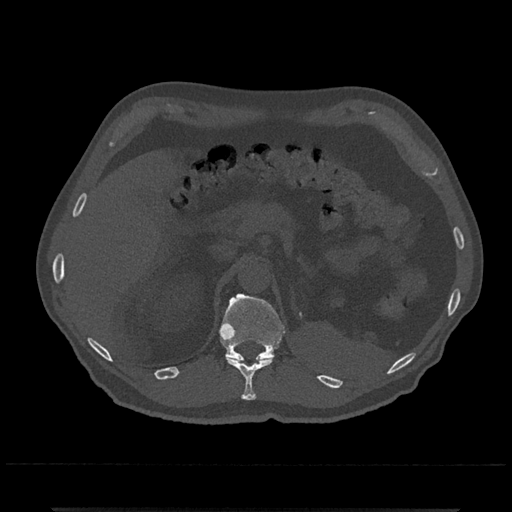
CT including the spine, one axial slice. Slice 457 of 797 in the series (ordered by position). Reconstruction kernel Br40s/3. Bone window (W 1800 / L 400 HU). 512 × 512 image matrix, field of view 393 × 393 mm. Patient: male, 67 years. From the clinical record (not read from this slice): primary cancer: prostate.
Annotated regions visible in this slice (semi-automatically segmented with operator editing):
- T11 vertebra: bounding box <225,356,274,400> (left, top, right, bottom; pixels)
- T12 vertebra: <219,293,286,361>